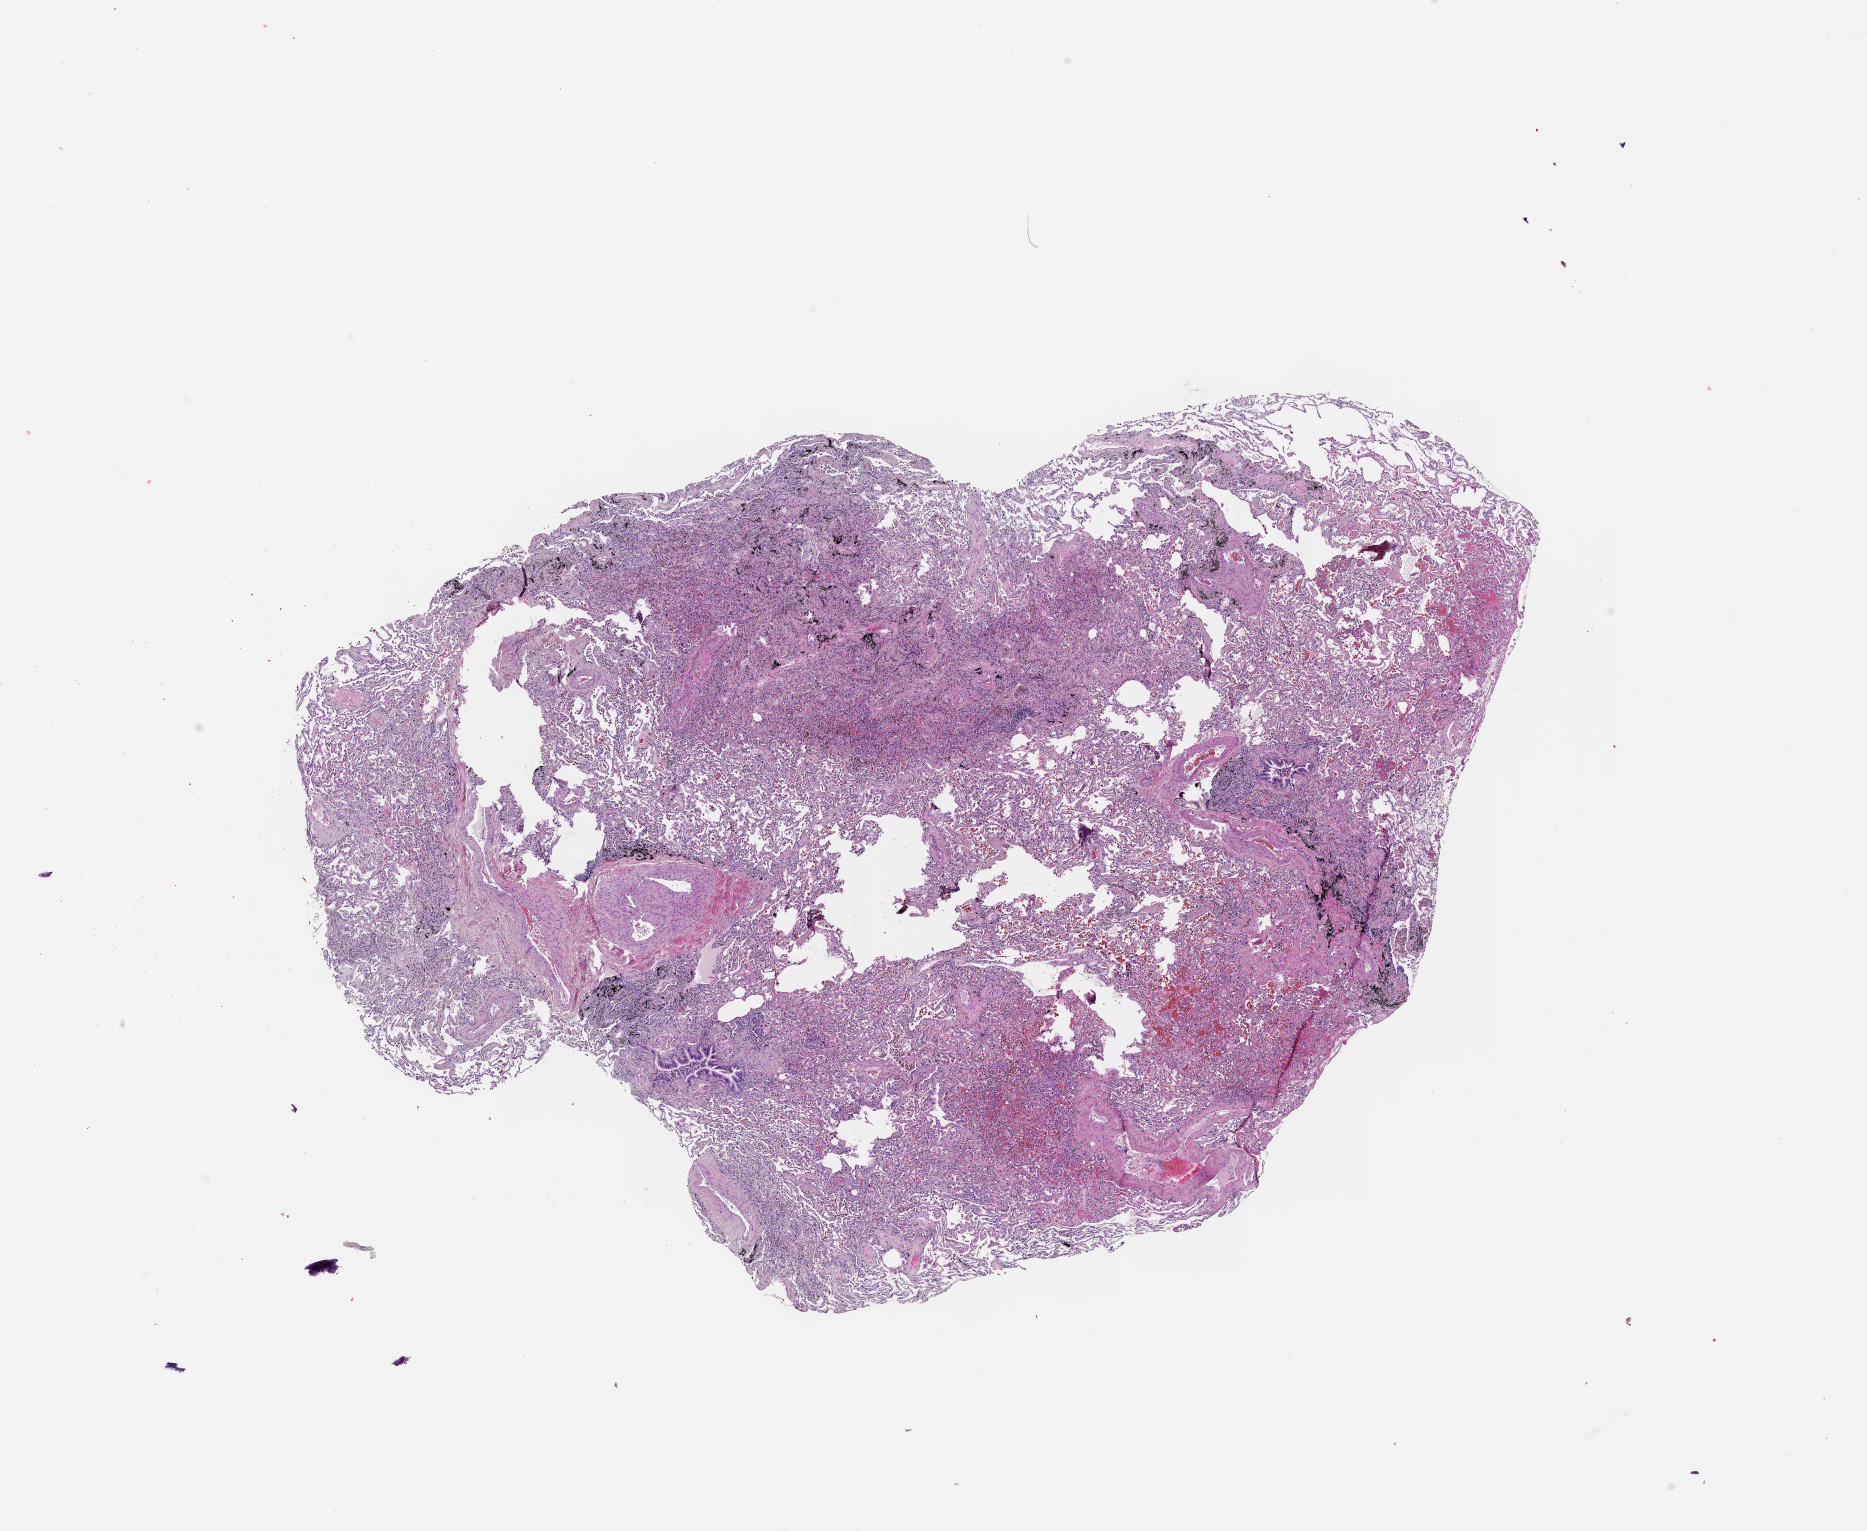
Hematoxylin and eosin (H&E) stained whole-slide image, a low-resolution overview of the entire scanned area, about 15.0 x 12.3 mm; lung, normal (non-tumour) tissue. 54-year-old male patient.
- this section: normal (non-tumour) tissue from the same patient
- patient diagnosis (cohort enrolment): squamous cell carcinoma (lung)